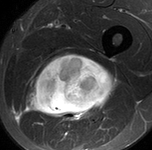
MRI of an extremity soft-tissue mass, one axial slice; slice 73 of 90 in the series (ordered by position); STIR; MR volume resampled by the dataset authors to the PET/CT grid (not the native acquisition matrix); 3.27 mm slice thickness; 152 × 150 image matrix, field of view 148 × 146 mm. Male patient. Case-level facts recorded for this patient, not image findings: histological type: undifferentiated pleomorphic liposarcoma; grade: high; site of the primary tumour: left thigh.
Structures marked on this image (expert contour drawn on MRI and transferred to this co-registered scan by the dataset authors):
- gross tumour volume including surrounding oedema: bounding box [x1, y1, x2, y2] px = [23, 53, 119, 124]
- gross tumour volume (mass): [34, 55, 117, 115]